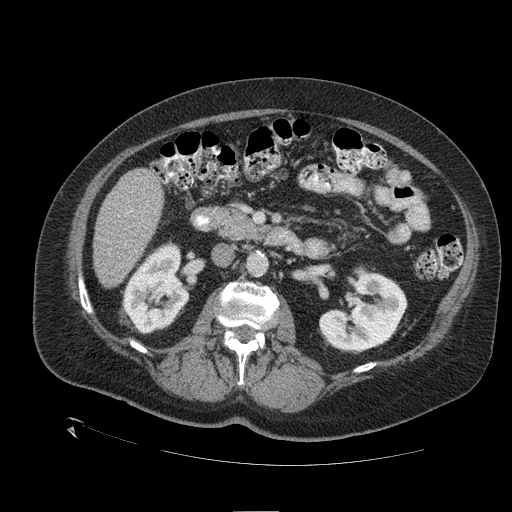
Contrast-enhanced abdominal CT (liver protocol), one axial slice; position 45 of 109 along the scan axis; reconstruction kernel STANDARD; 120 kVp; one of 2 acquisitions stored at this slice position; soft-tissue window (W 400 / L 40 HU); 2.5 mm slice thickness; 512 × 512 image matrix. From the clinical record (not read from this slice): diagnosis: hepatocellular carcinoma (patient treated with transarterial chemoembolisation; whether this scan precedes or follows treatment is not stated here); TNM stage (as recorded): Stage-I; Child-Pugh class: A; tumour differentiation: no biopsy; tumour nodularity: uninodular.
Annotated regions visible in this slice (semi-automatically segmented with operator editing):
- liver parenchyma outside the tumour (the mass and vessels are separate outlines, so this box may not span the whole liver): bounding box (x1, y1, x2, y2) in pixels: (92, 168, 164, 286)